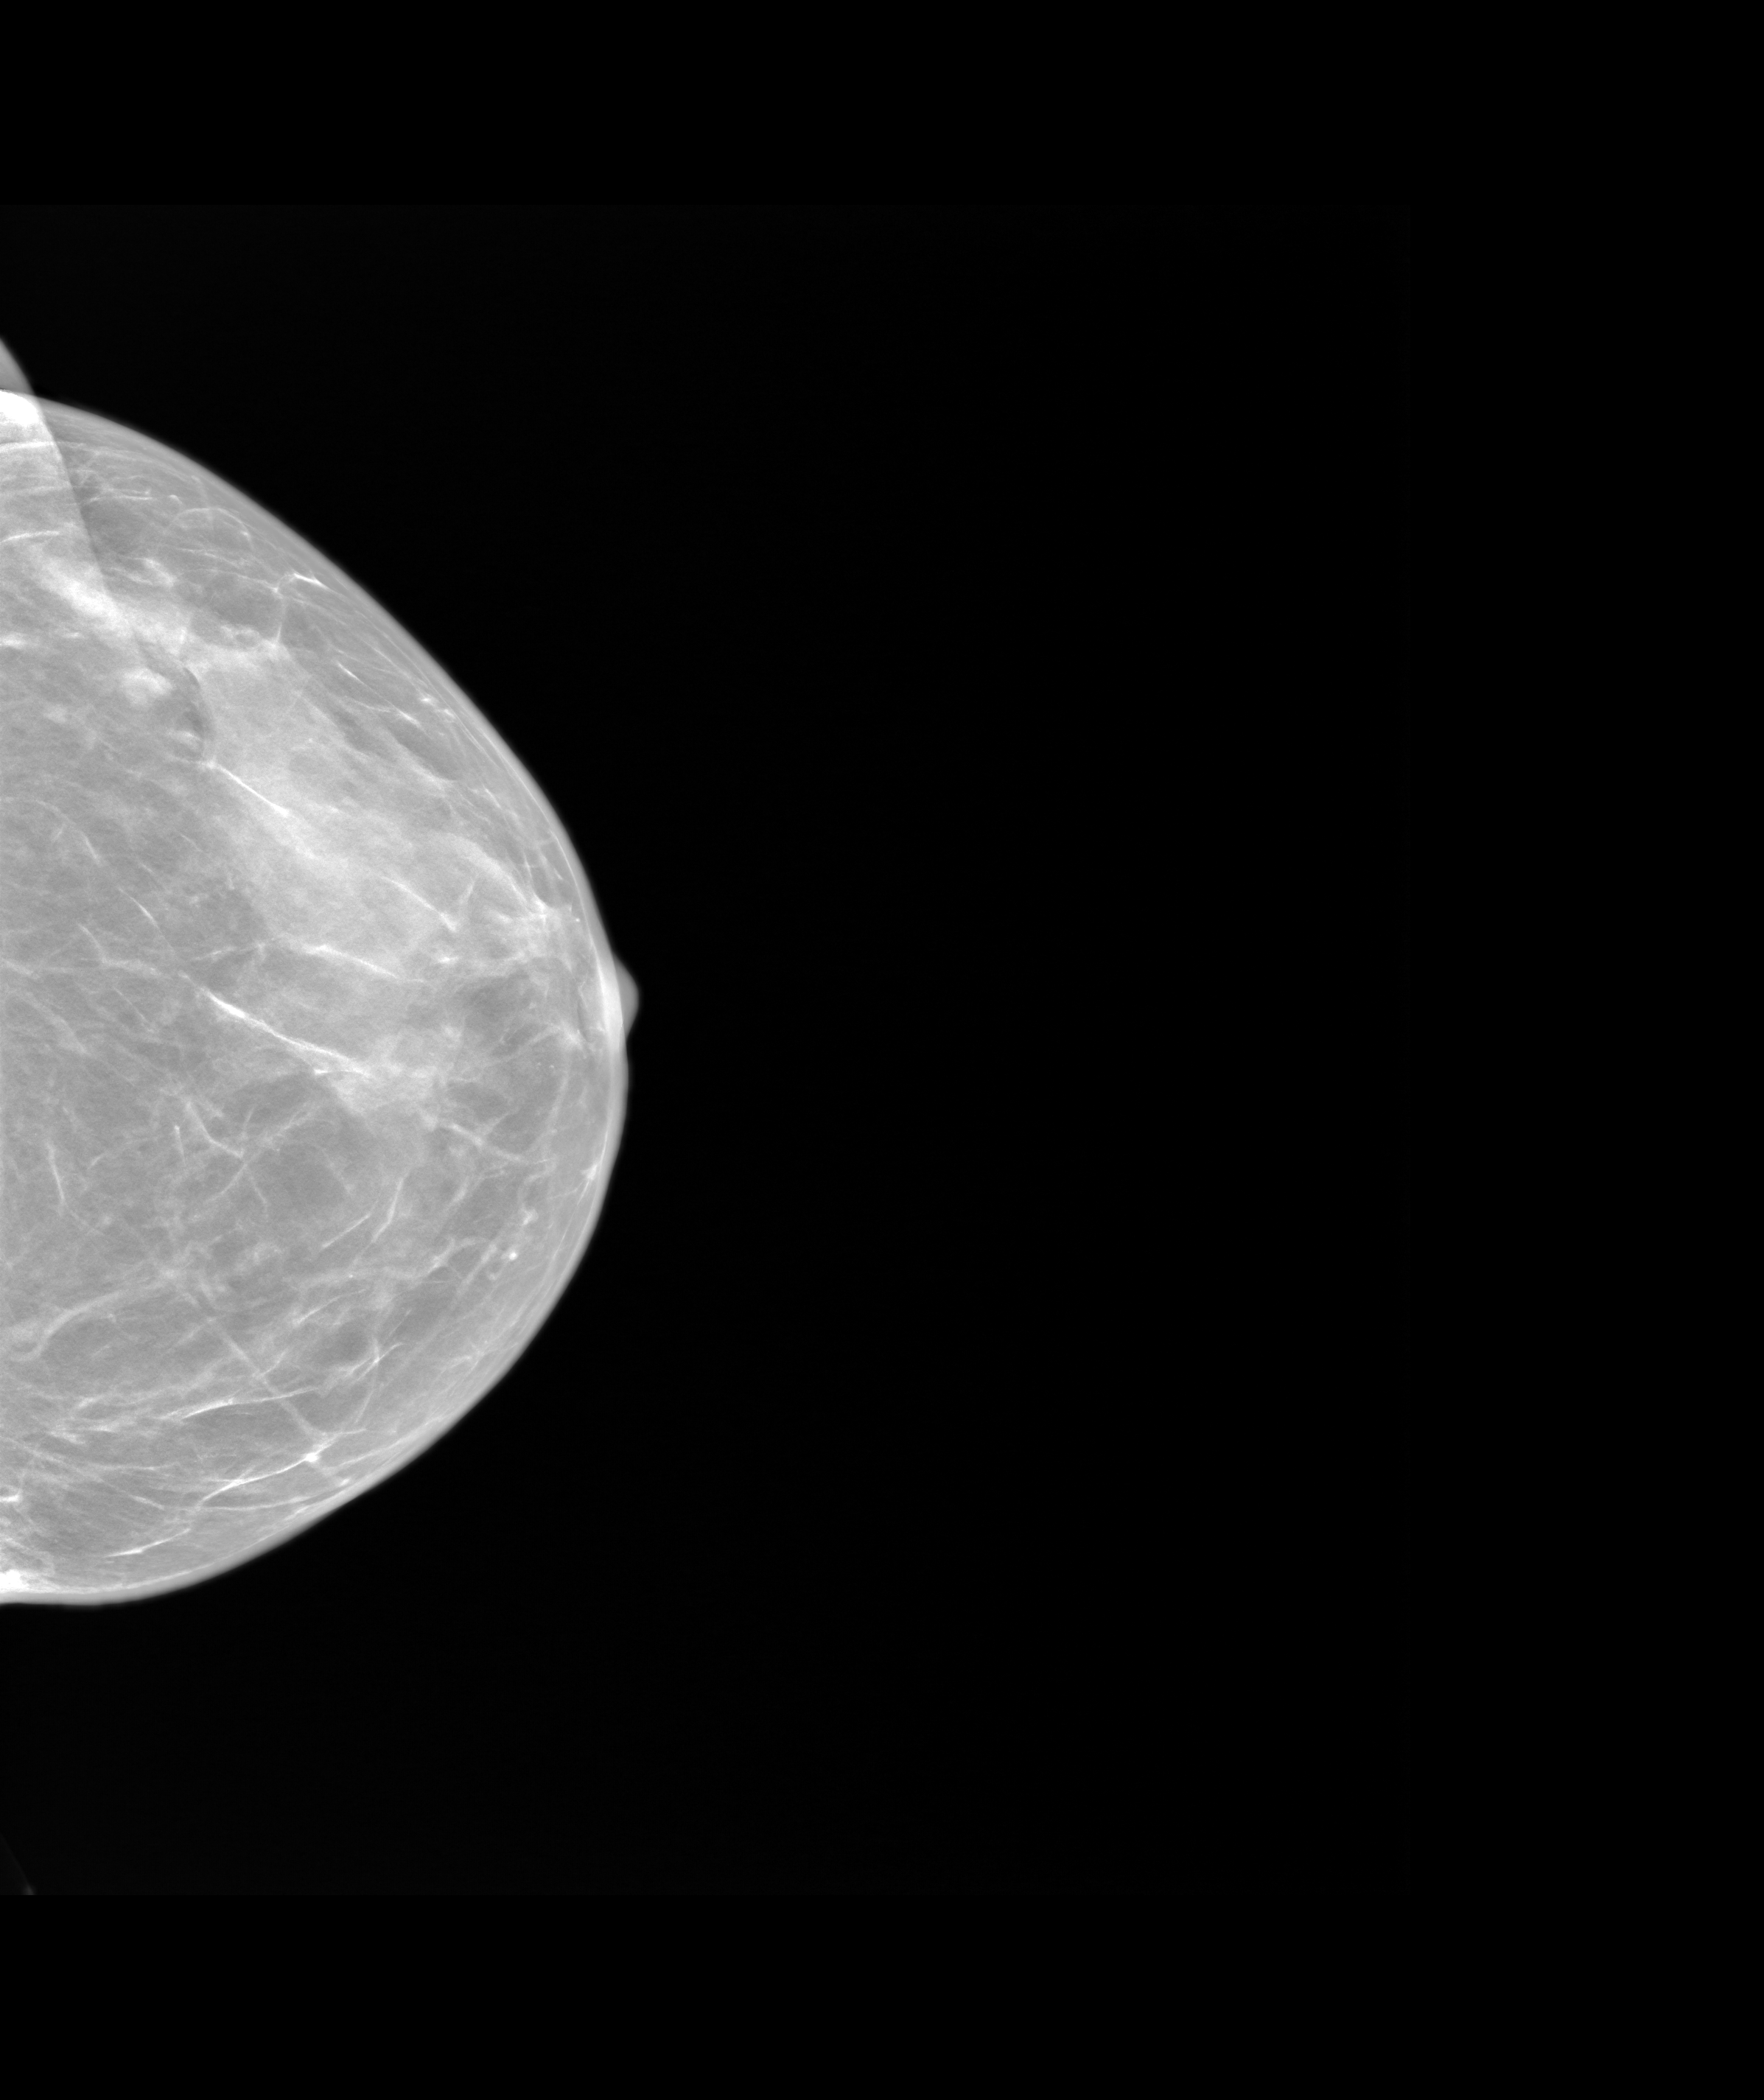
Annual screening mammography examination. Female patient, age 48 years.
Image type: synthesized 2-D view from tomosynthesis. Breast: left. Projection: cranio-caudal projection.